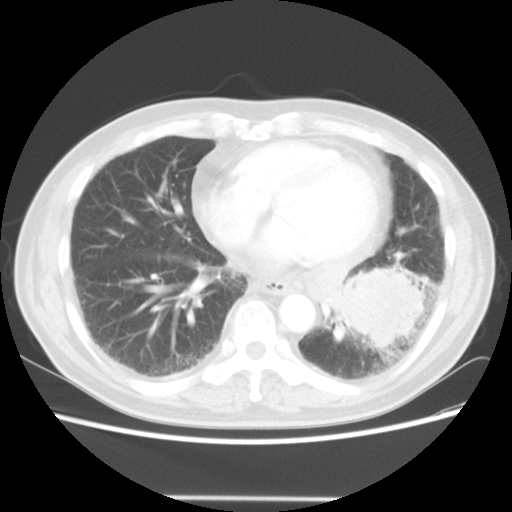
Chest CT, one axial slice; position 18 of 56 along the scan axis; lung window (W 1500 / L -600 HU); 5 mm slice thickness; 512 × 512 image matrix, field of view 360 × 360 mm. Patient: male, 66 years. From the clinical record (not read from this slice): clinical TNM (as recorded): T4 N3 M0.
Outlined on this slice (rectangle marked by the reading radiologist):
- lung tumour (recorded histology: small cell carcinoma): bounding box (x1, y1, x2, y2) in pixels: (336, 253, 433, 362)